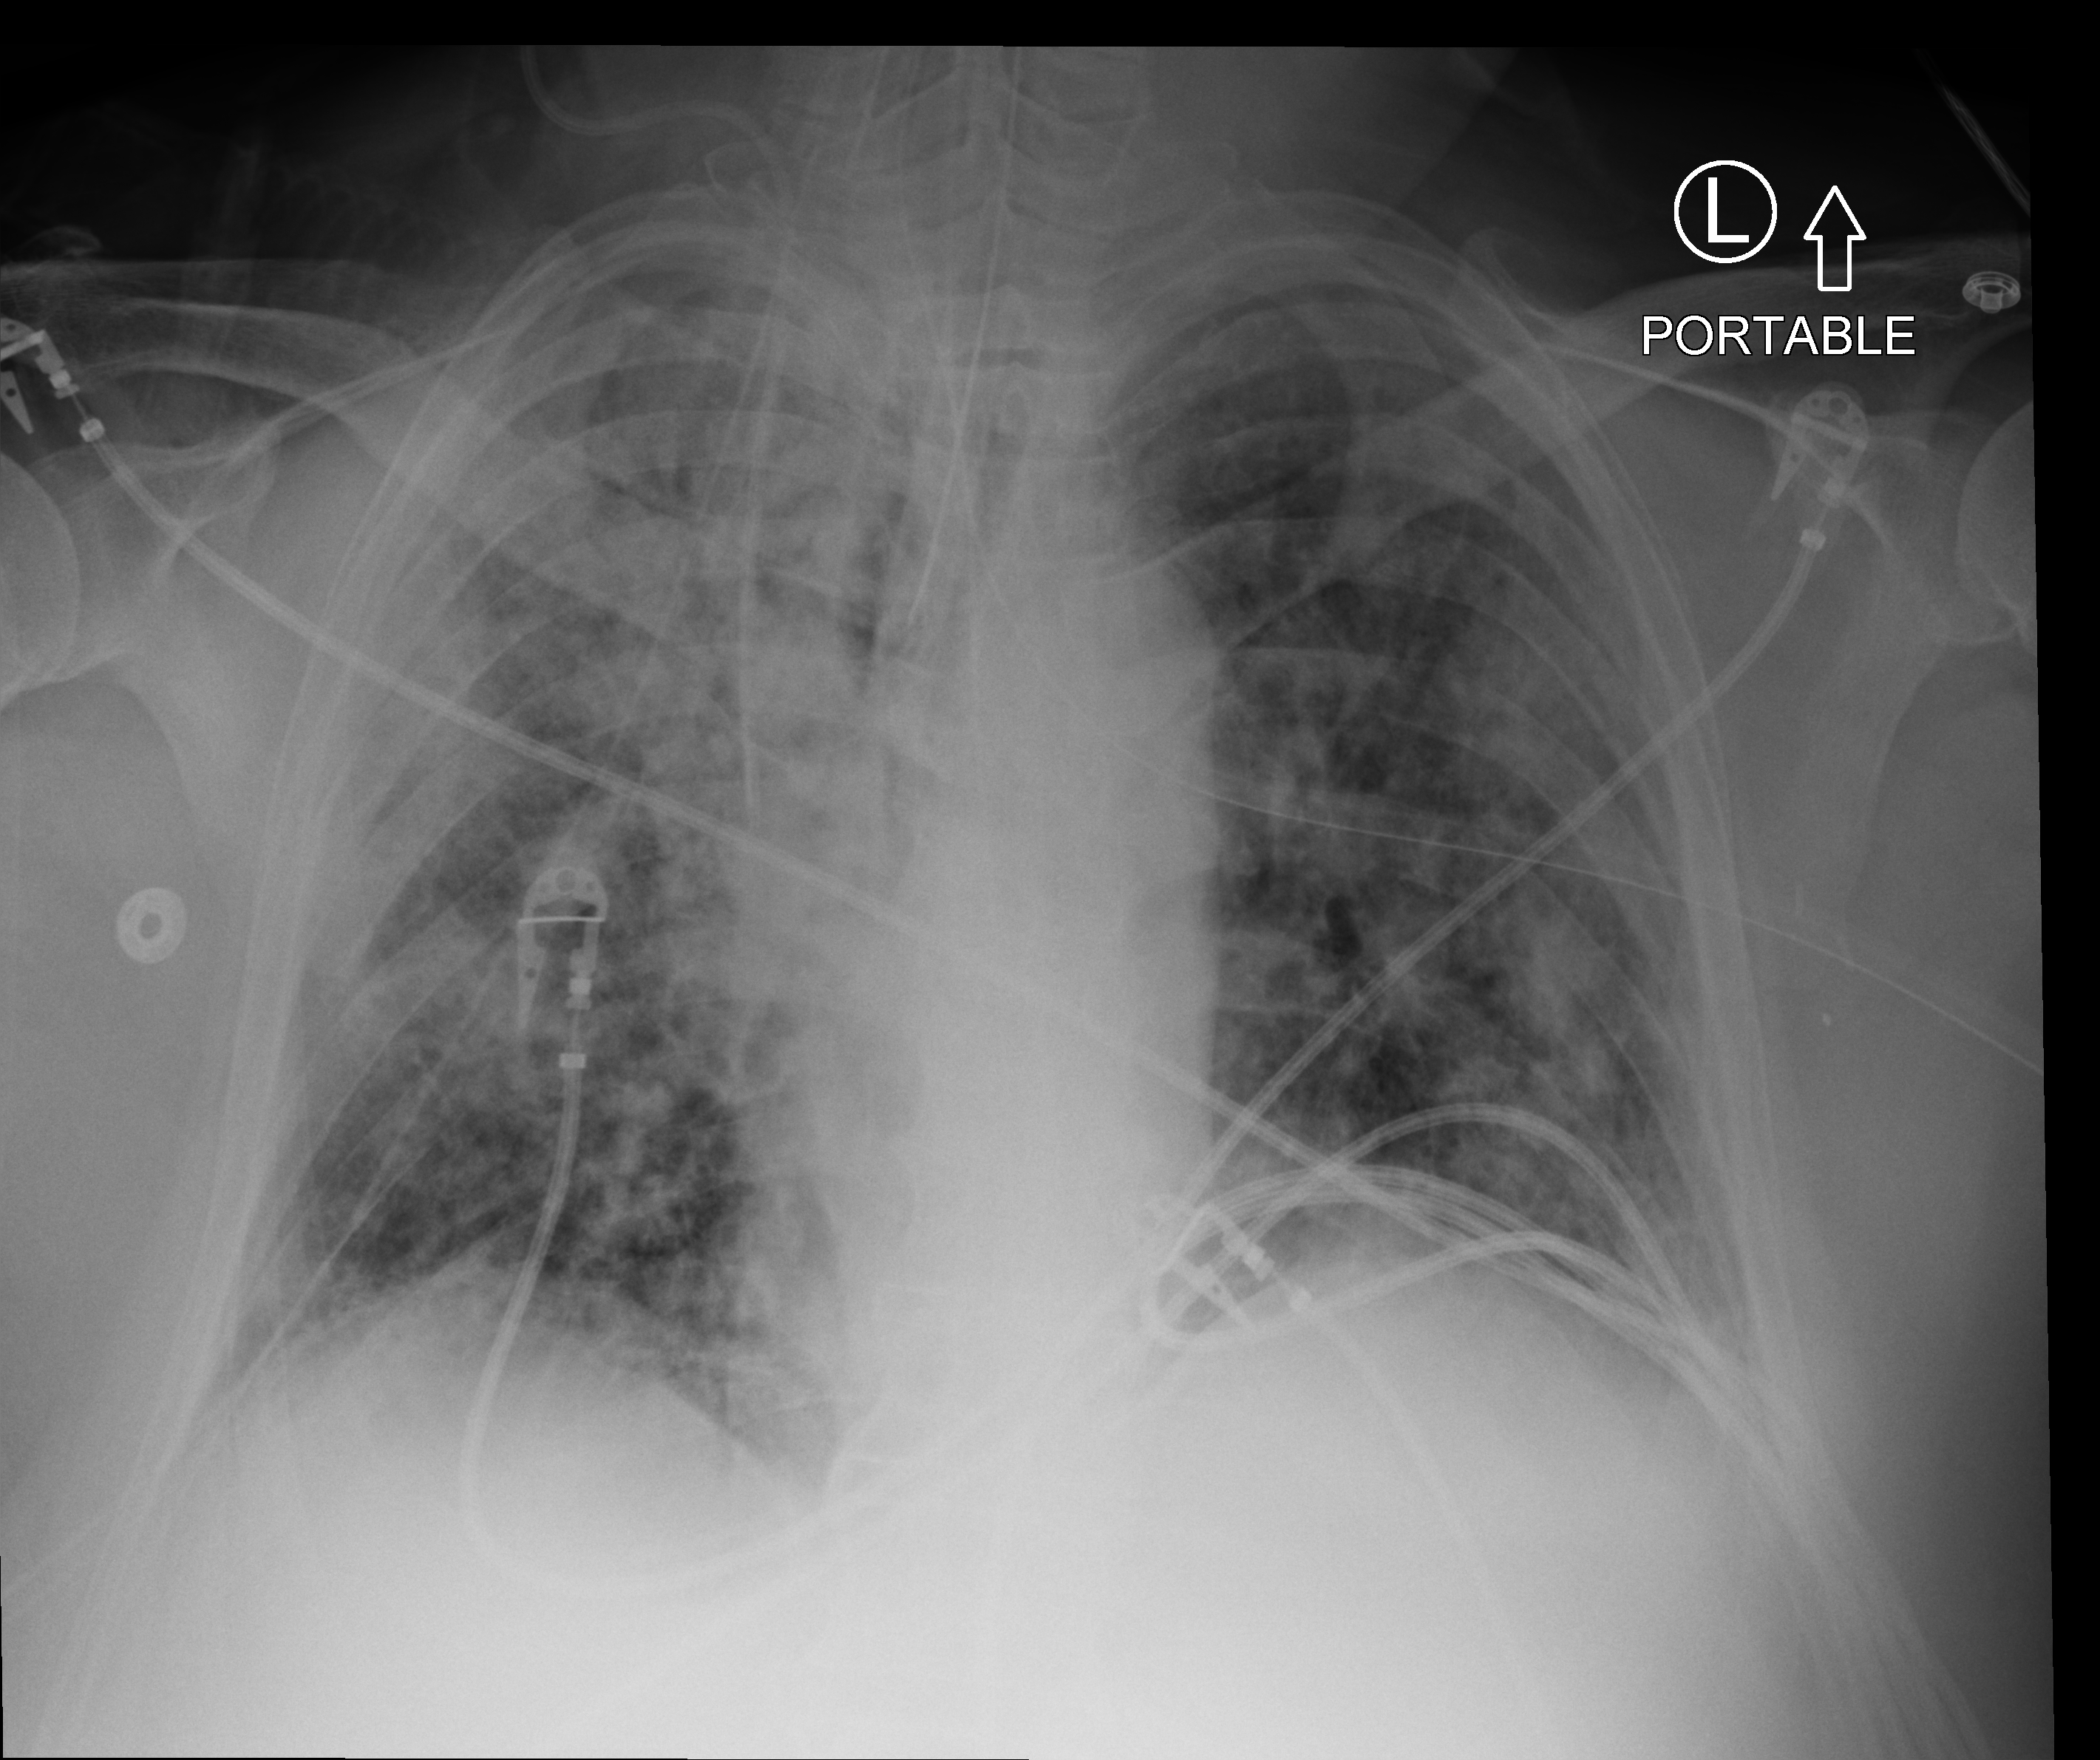
Bedside chest radiograph (computed radiography), anteroposterior (AP) projection. Patient hospitalised with COVID-19; male, aged 60–74 years.
From the hospital-stay record, not from the radiograph (when in the stay this image was taken is not recorded):
- length of hospital stay: 17 days
- mechanically ventilated during this hospital stay: yes